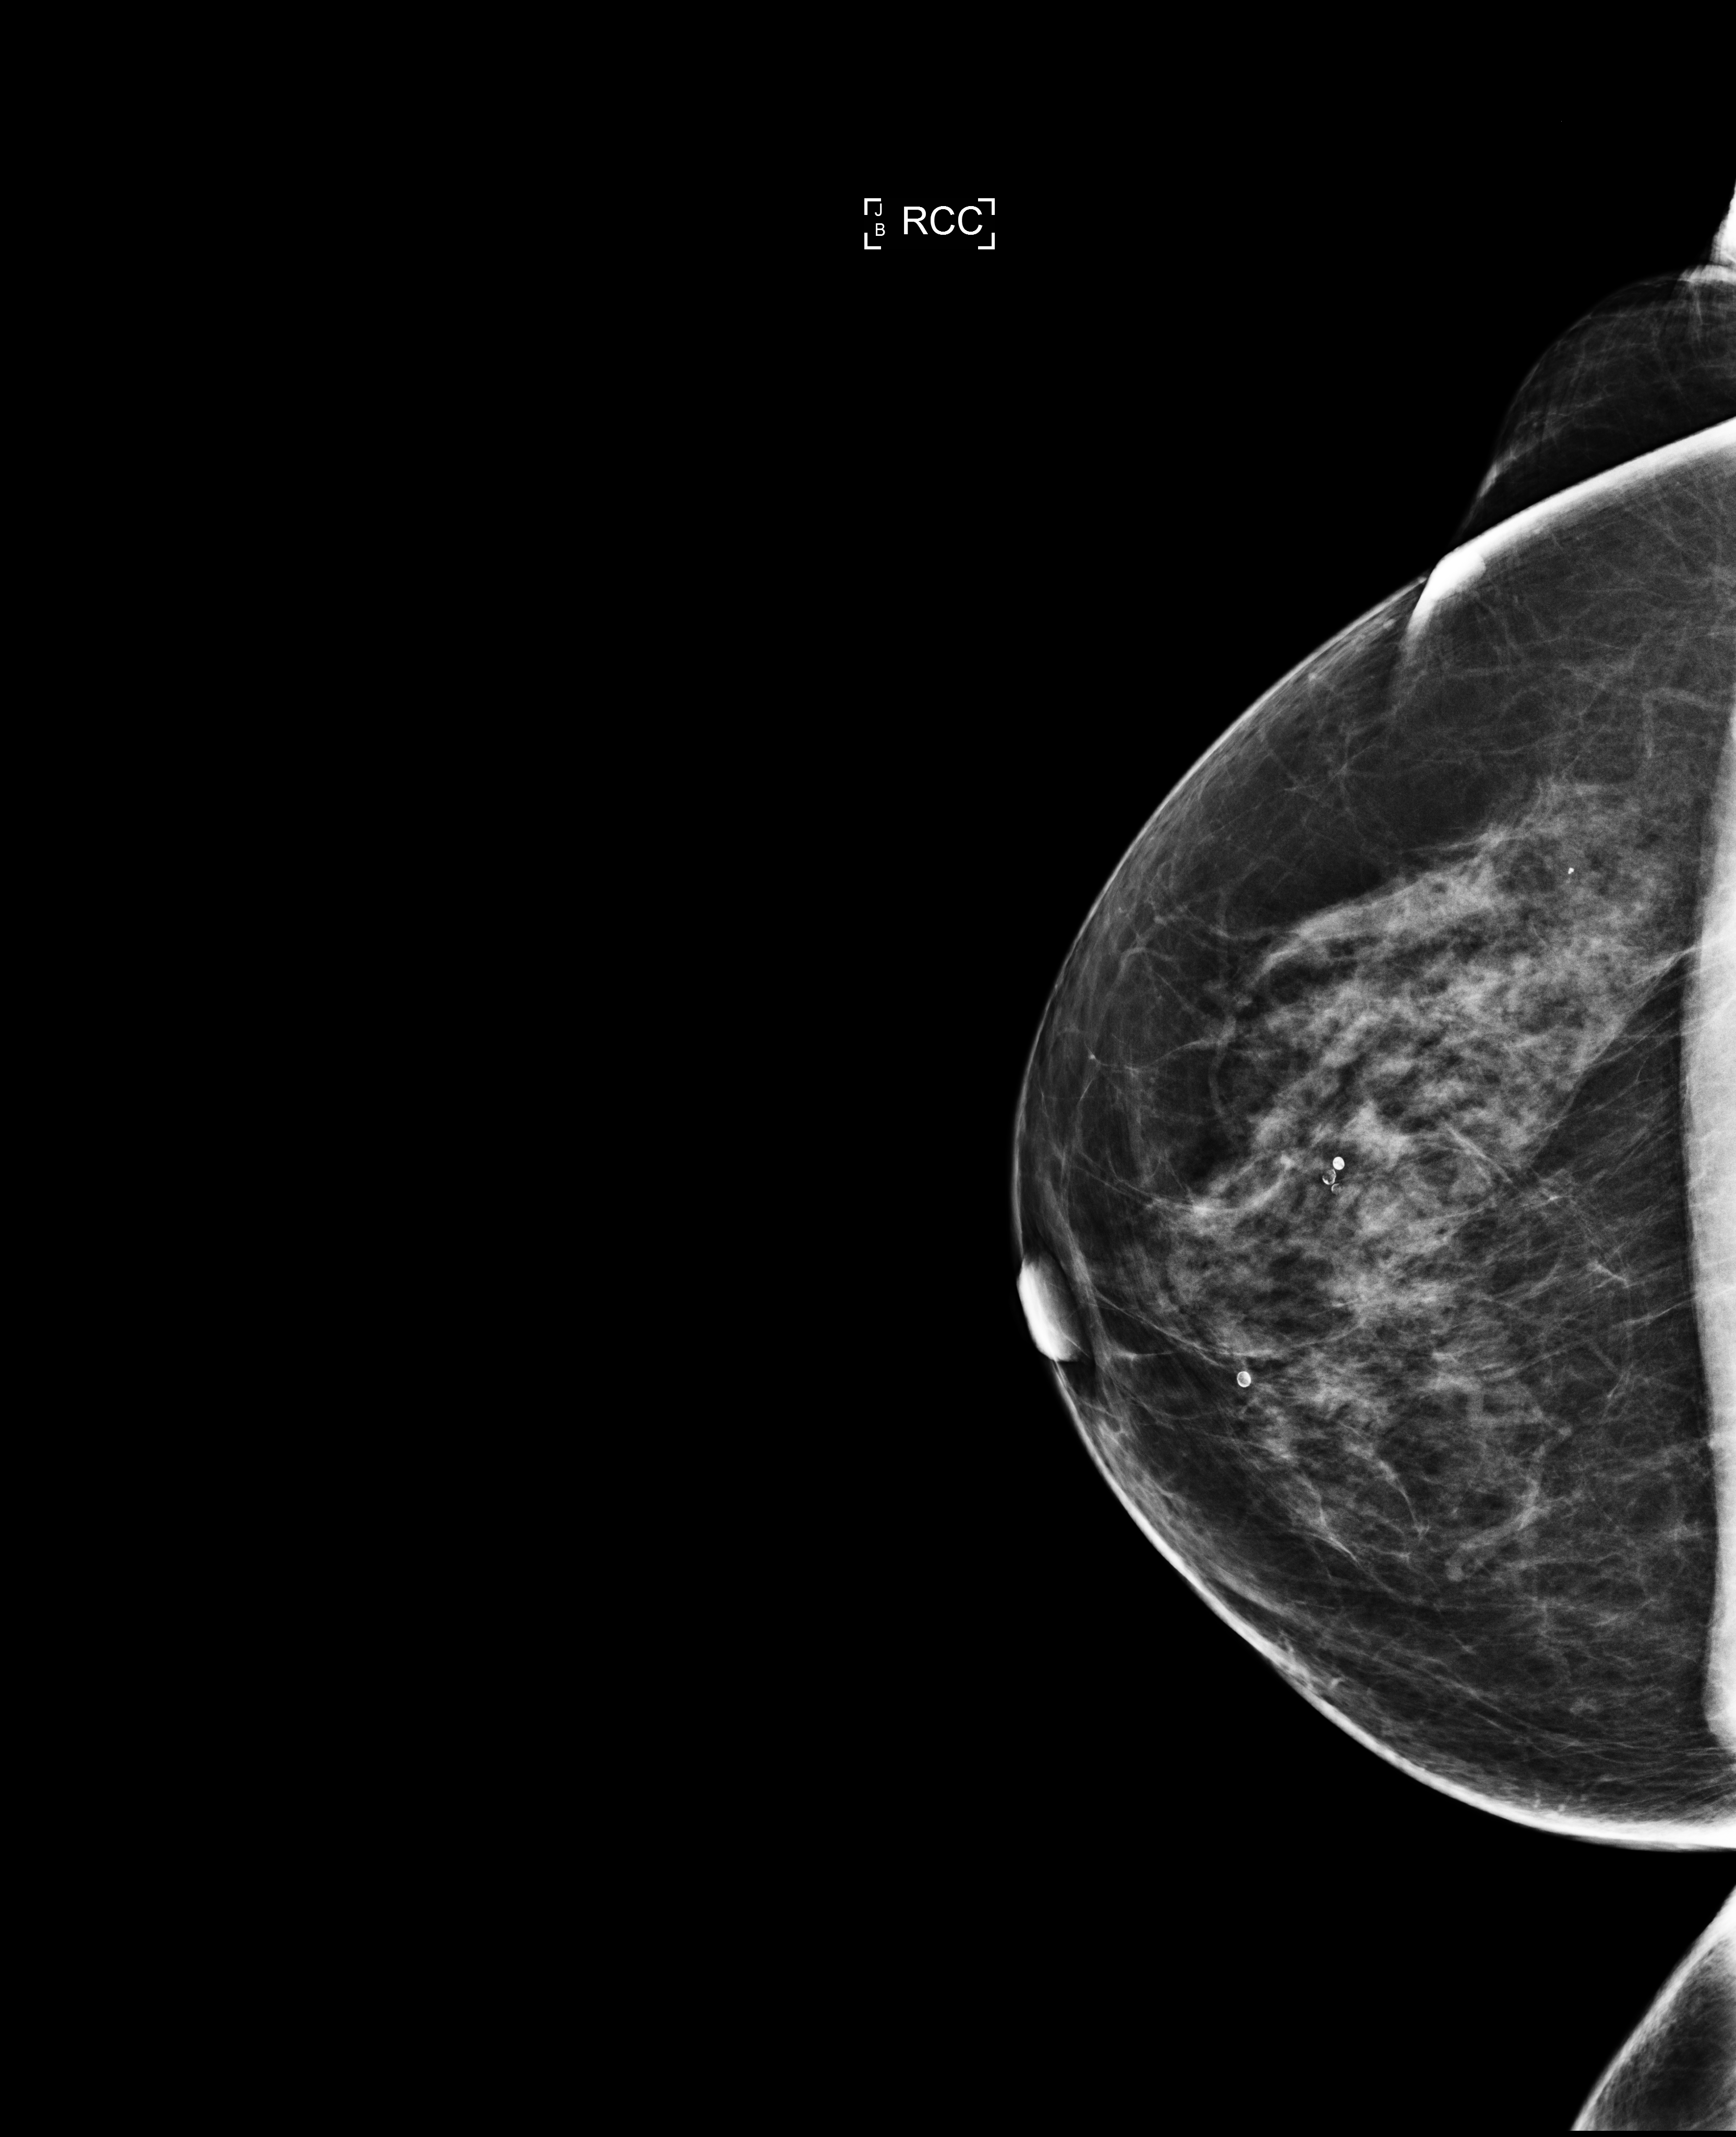
Digital mammogram (FFDM), right breast, CC view, annual screening mammography examination, compressed breast thickness 68 mm. Patient: female, 63 years.
- BI-RADS breast density category at the screening exam (both breasts, scale 1–4): 2
- final BI-RADS category for the screening round (tomosynthesis exam, both breasts): category 1
- recall: no recall after this screen